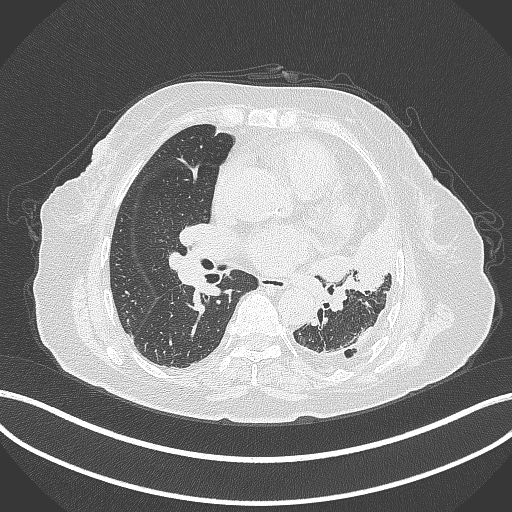
Chest CT, one axial slice. Slice 185 of 399 in the series (ordered by position). Reconstruction kernel B70f. Lung window (W 1500 / L -600 HU). 1 mm slice thickness. 512 × 512 image matrix, field of view 400 × 400 mm. Patient: female, 75 years. Case-level facts recorded for this patient, not image findings: clinical TNM (as recorded): T3 N3 M1.
Annotated regions visible in this slice (rectangle marked by the reading radiologist):
- lung tumour (recorded histology: adenocarcinoma): bounding box <311,215,396,293> (left, top, right, bottom; pixels)